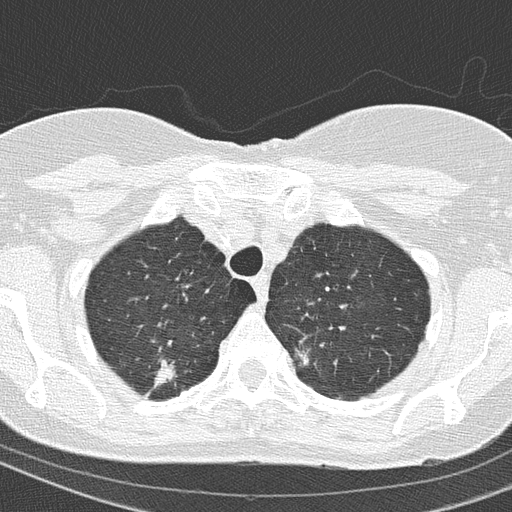
Low-dose screening chest CT, one axial slice; slice 129 of 154 in the series (ordered by position); reconstruction kernel B50f; 120 kVp; lung window (W 1500 / L -600 HU); 2 mm slice thickness; 512 × 512 image matrix.
Structures marked on this image (outlined manually by an expert reader):
- lesion 1 (tumor, upper lobe of right lung): bounding box <145,358,178,397> (left, top, right, bottom; pixels)